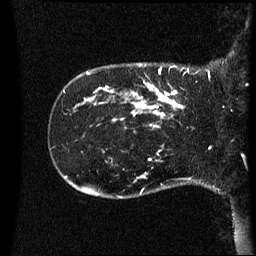
Breast MRI (dynamic contrast-enhanced), one sagittal slice; position 9 of 60 along the scan axis; dynamic contrast-enhanced series, image 2 of 3 at this slice position (ordered by acquisition); 1.5 T; TE 4.2 ms, TR 8.4 ms; 256 × 256 image matrix, field of view 220 × 220 mm. Female patient, age 41 years. Case-level facts recorded for this patient, not image findings: setting: breast cancer imaged before/during neoadjuvant chemotherapy; receptor status: HER2-positive.
Annotated regions visible in this slice (semi-automatic segmentation, software-assisted and operator-edited):
- analysis volume of interest (the breast-tissue region the enhancement analysis was run in; not a lesion): bounding box (x1, y1, x2, y2) in pixels: (122, 80, 187, 125)
- tumour enhancement mask (voxels above the 70 % enhancement threshold inside the analysis volume of interest): (133, 84, 184, 117)